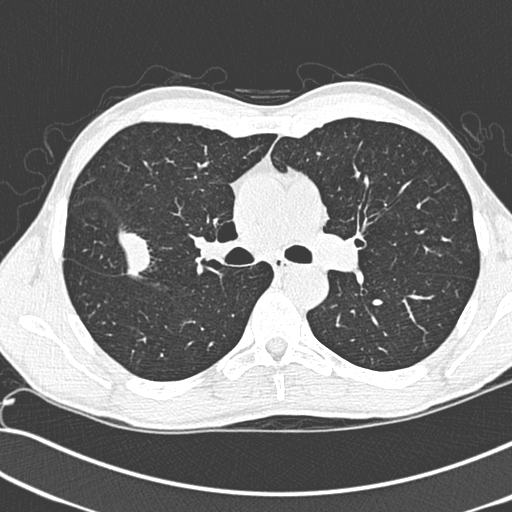
Low-dose screening chest CT, one axial slice. Slice 186 of 281 in the series (ordered by position). 120 kVp. Lung window (W 1500 / L -600 HU). 1.3 mm slice thickness. 512 × 512 image matrix.
Annotated regions visible in this slice (manually delineated by an expert):
- lesion 1 (tumor, upper lobe of right lung): bounding box [x1, y1, x2, y2] px = [118, 231, 154, 278]